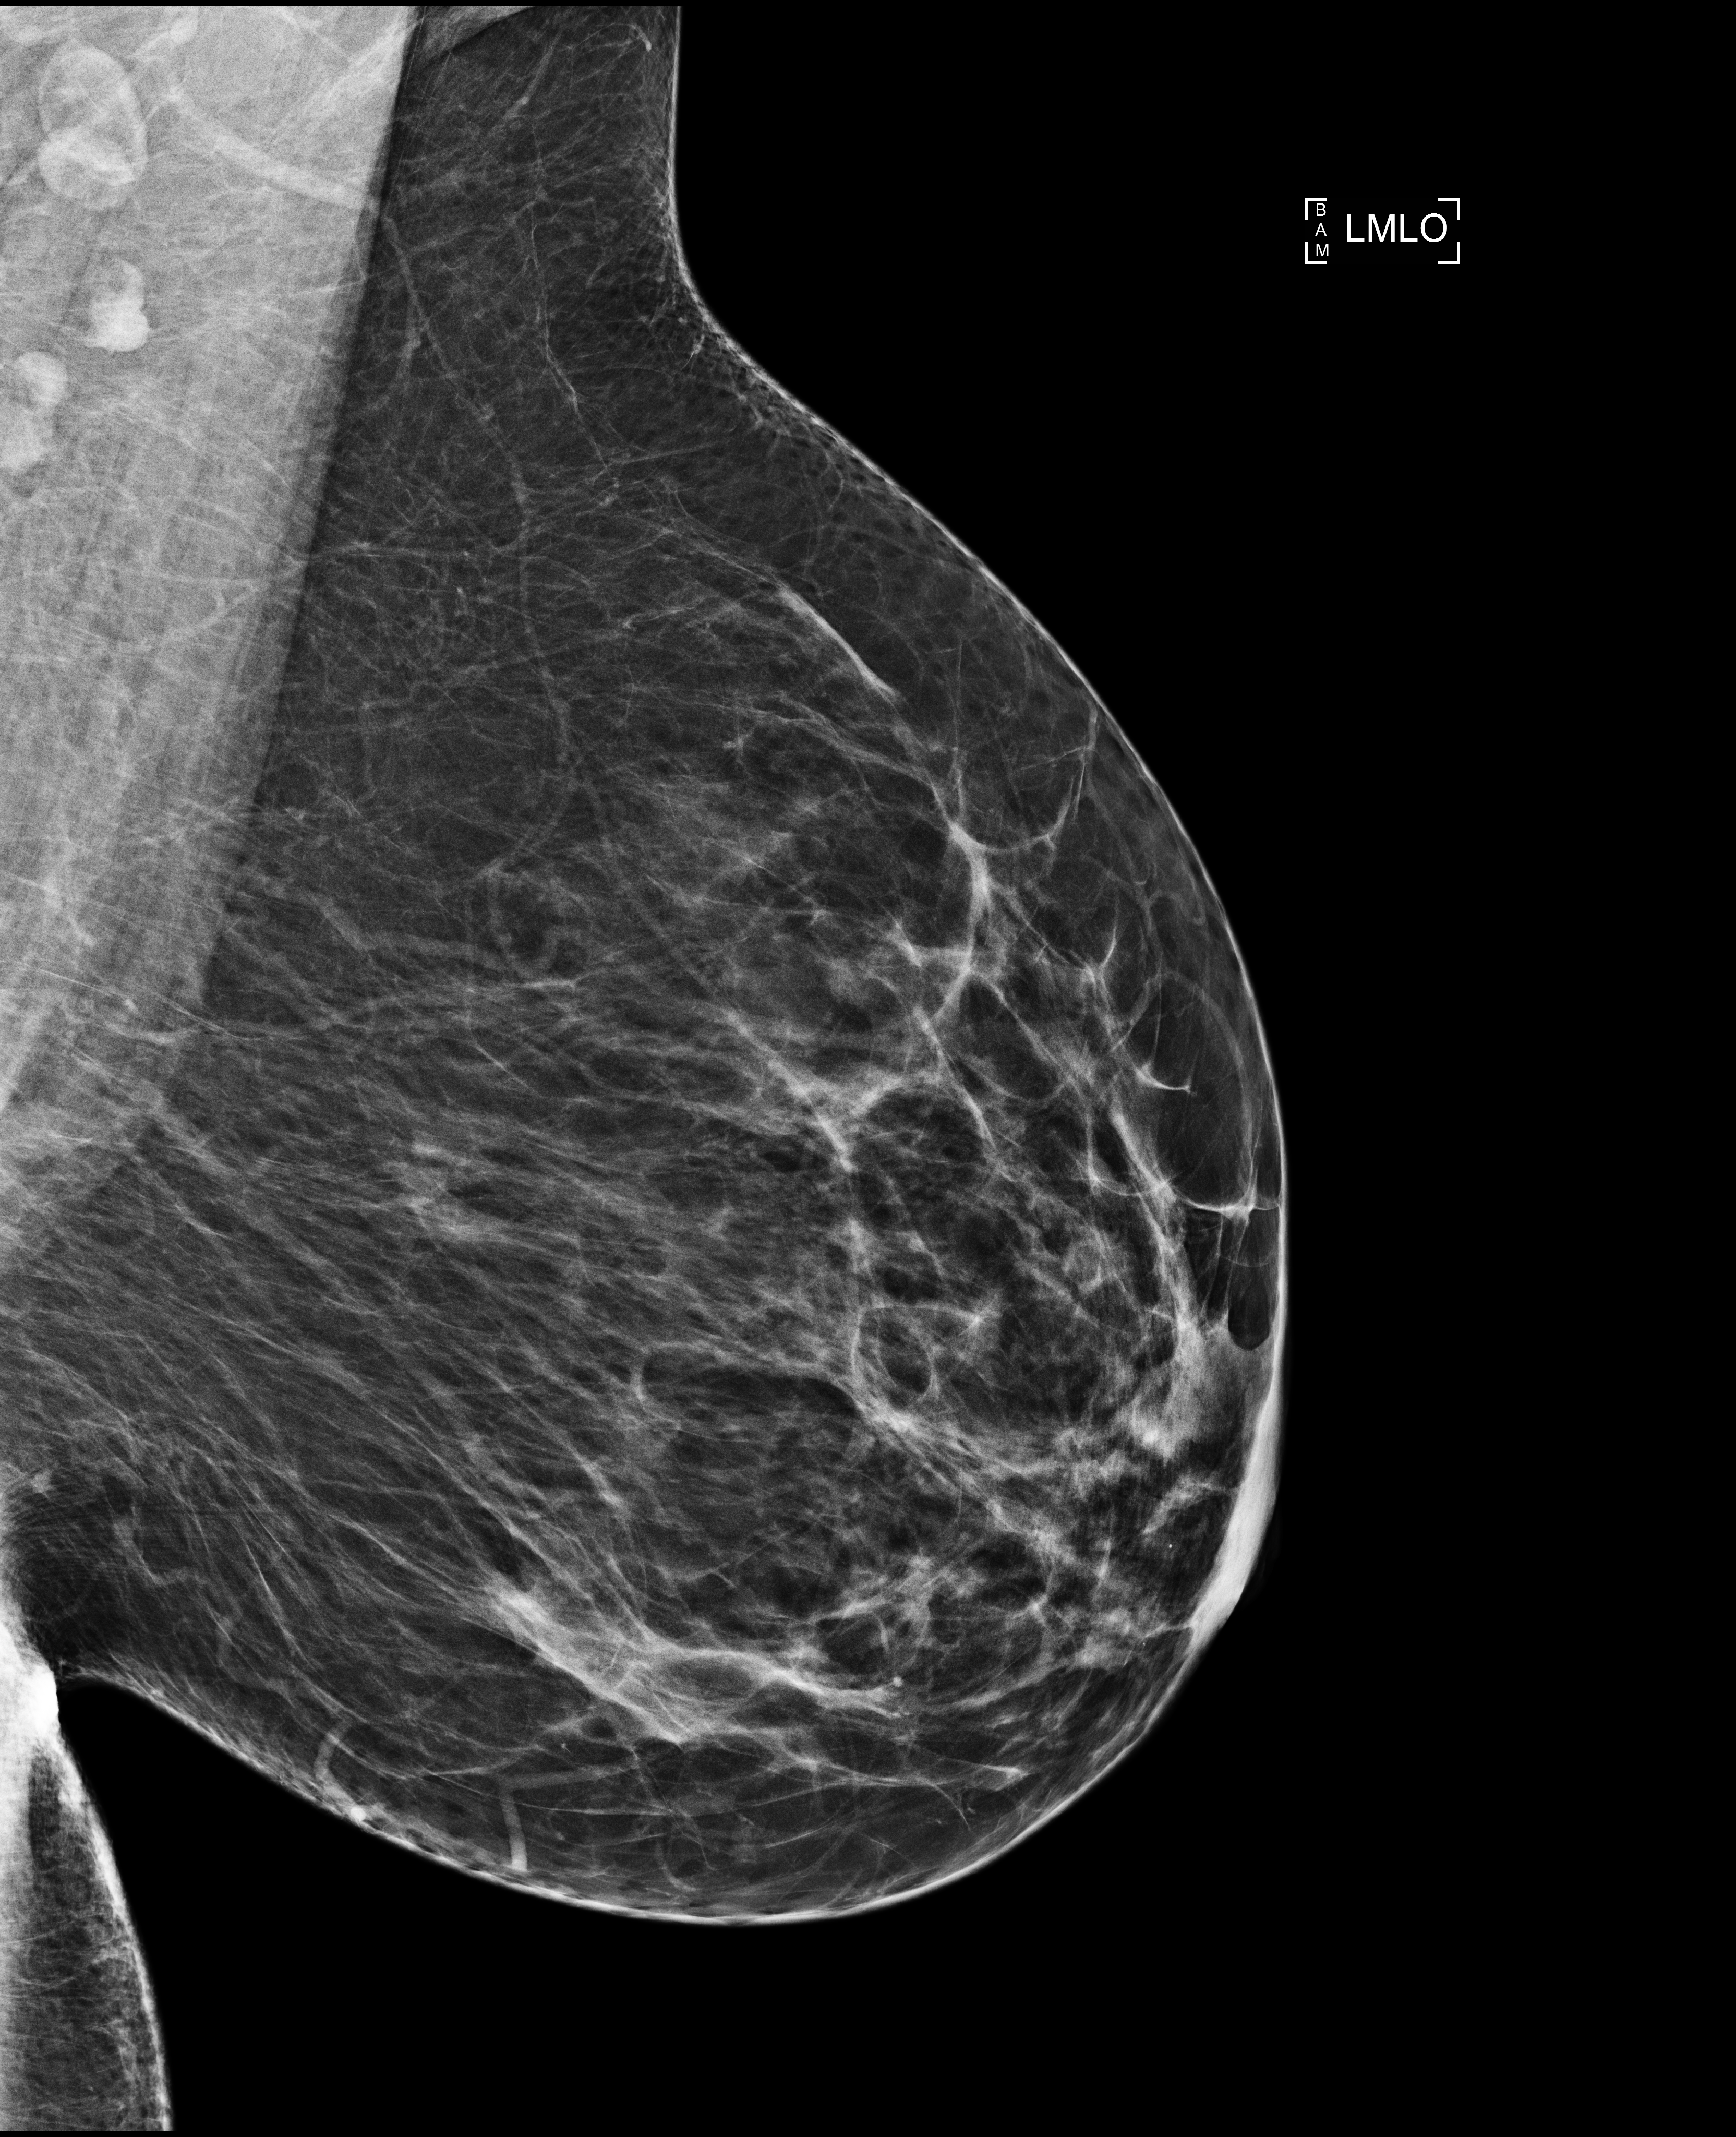
Annual screening mammography examination; compressed breast thickness 66 mm; system: Selenia Dimensions. Patient: female, 47 years.
Image type: full-field digital mammogram. Breast: left. Projection: mediolateral oblique (MLO) view.